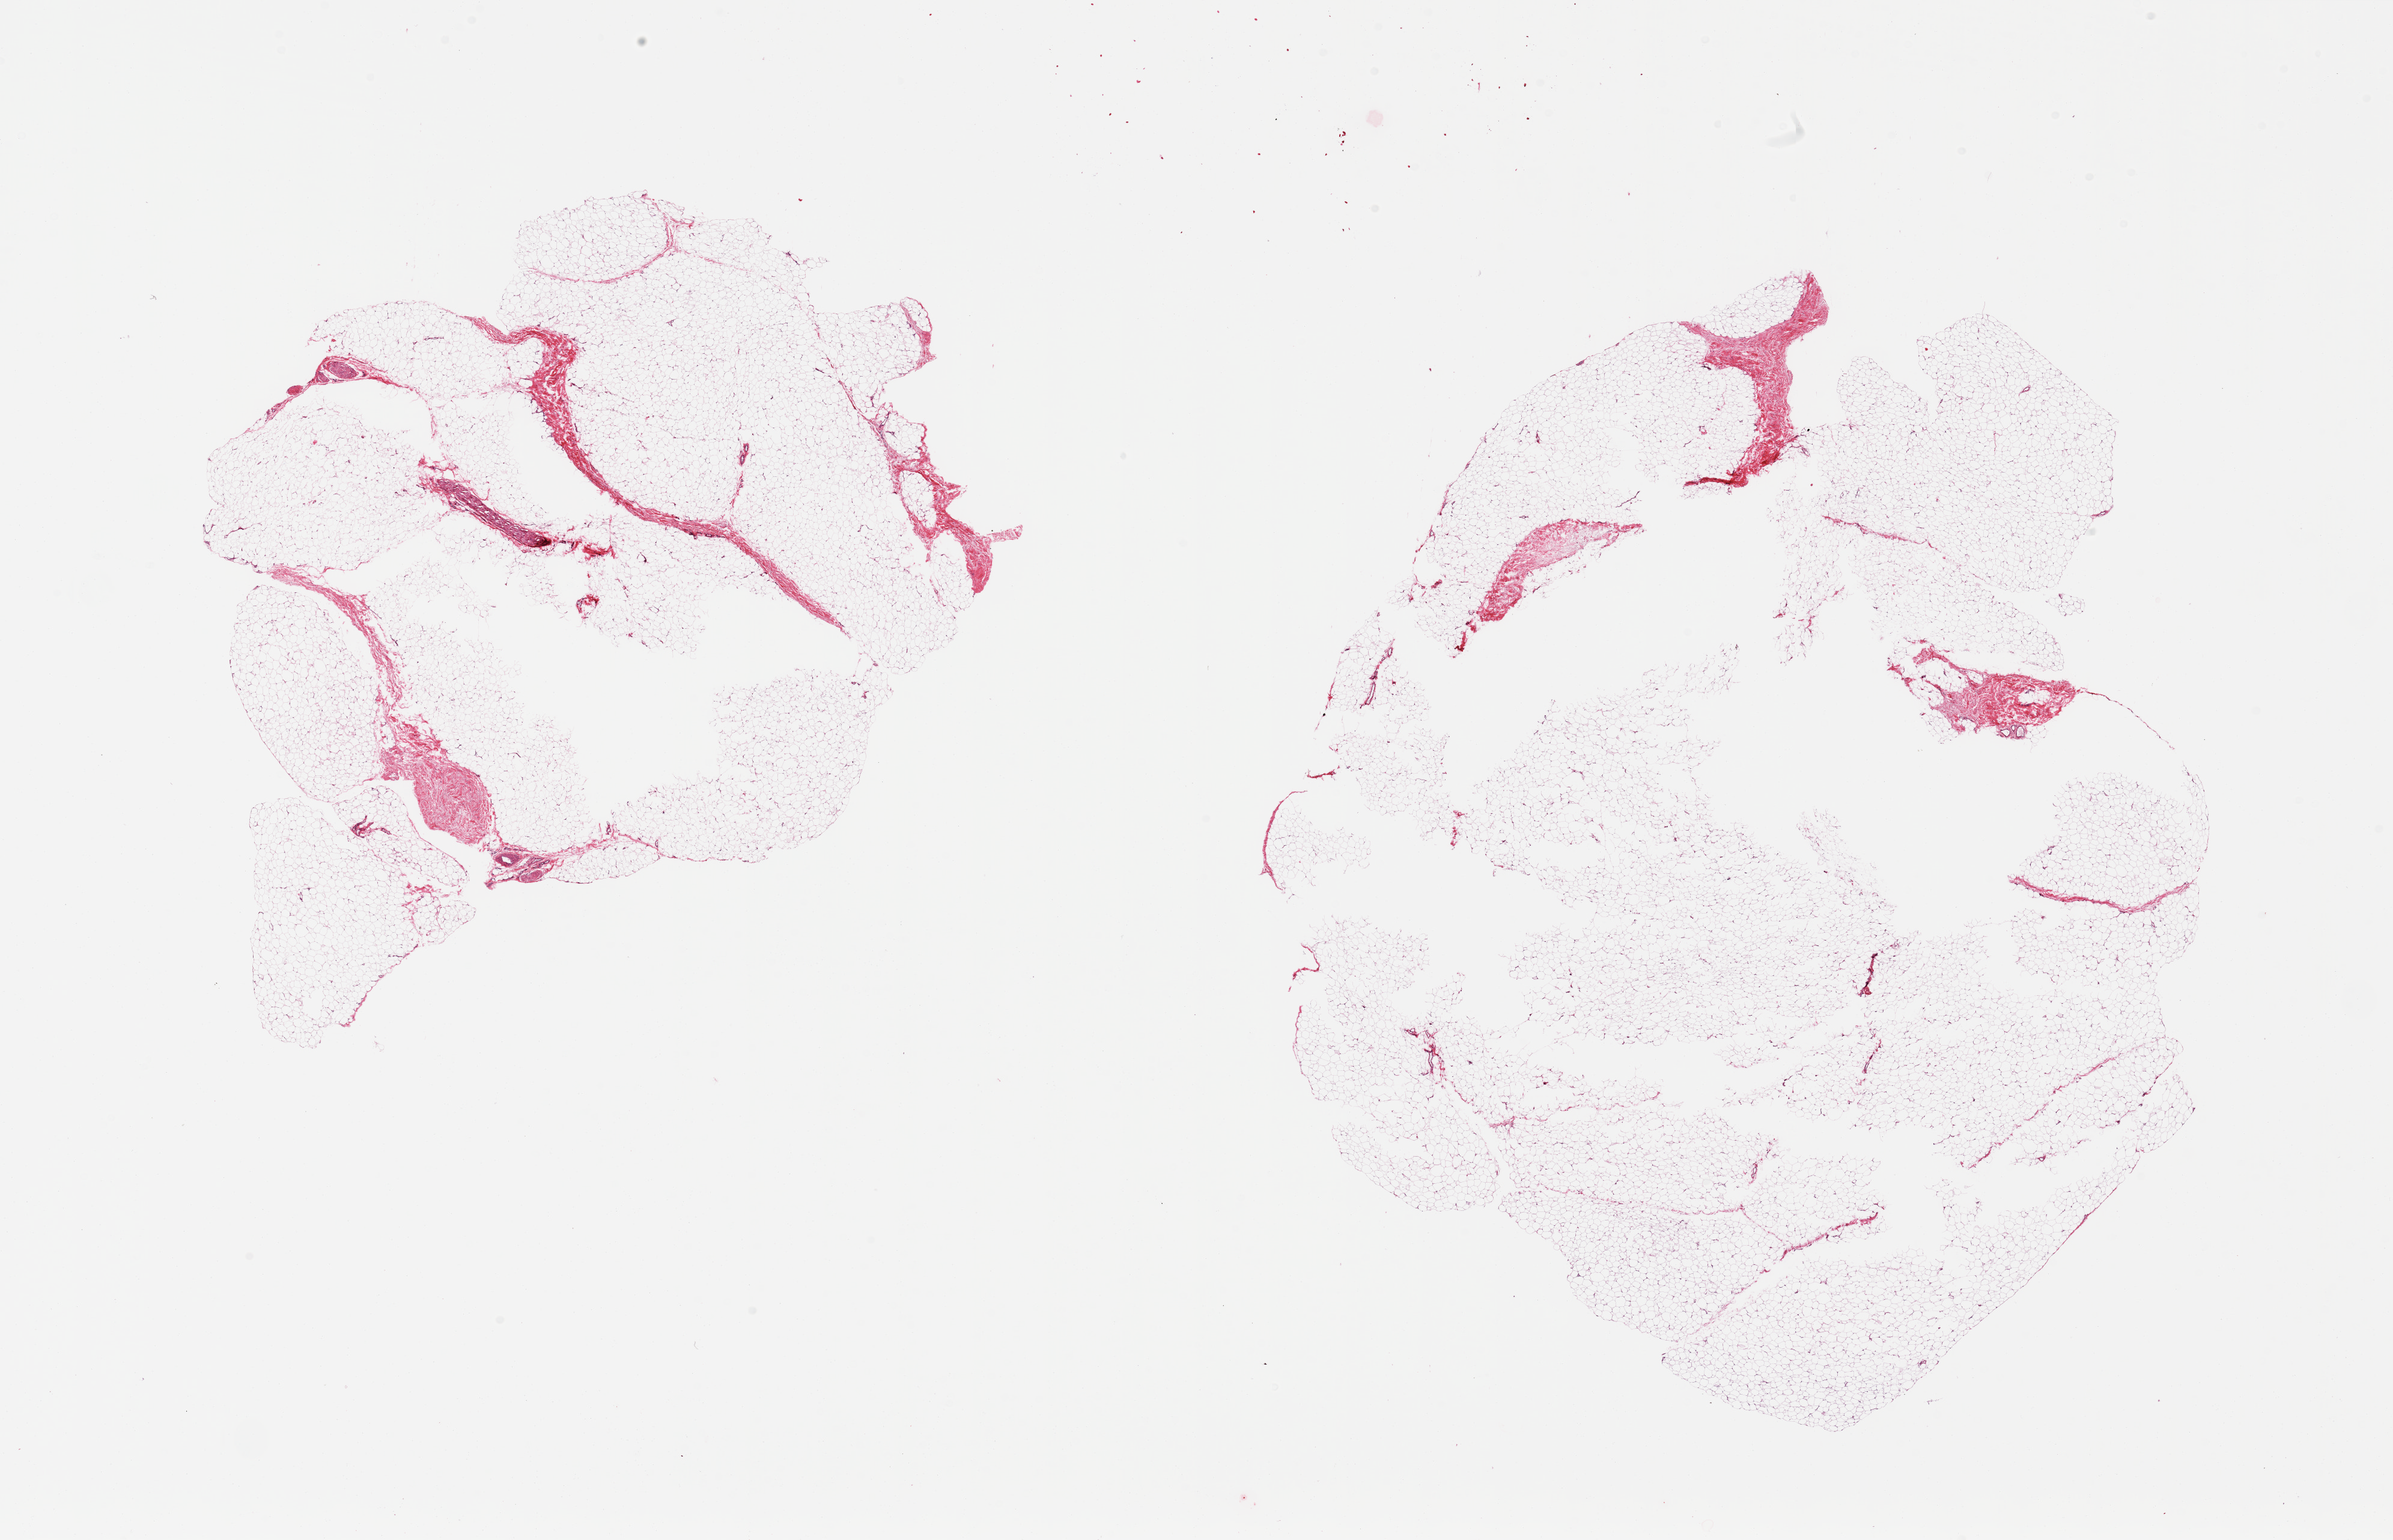
Whole-slide image, haematoxylin and eosin stain, brightfield — a low-resolution overview of the entire scanned area, about 31.5 x 20.3 mm, PAXgene-fixed paraffin-embedded (PFPE) section, target tissue: adipose tissue, tissue donor sample. Female donor.
Pathologist's review note for this sample: 2 pieces; <5% fibrous content.